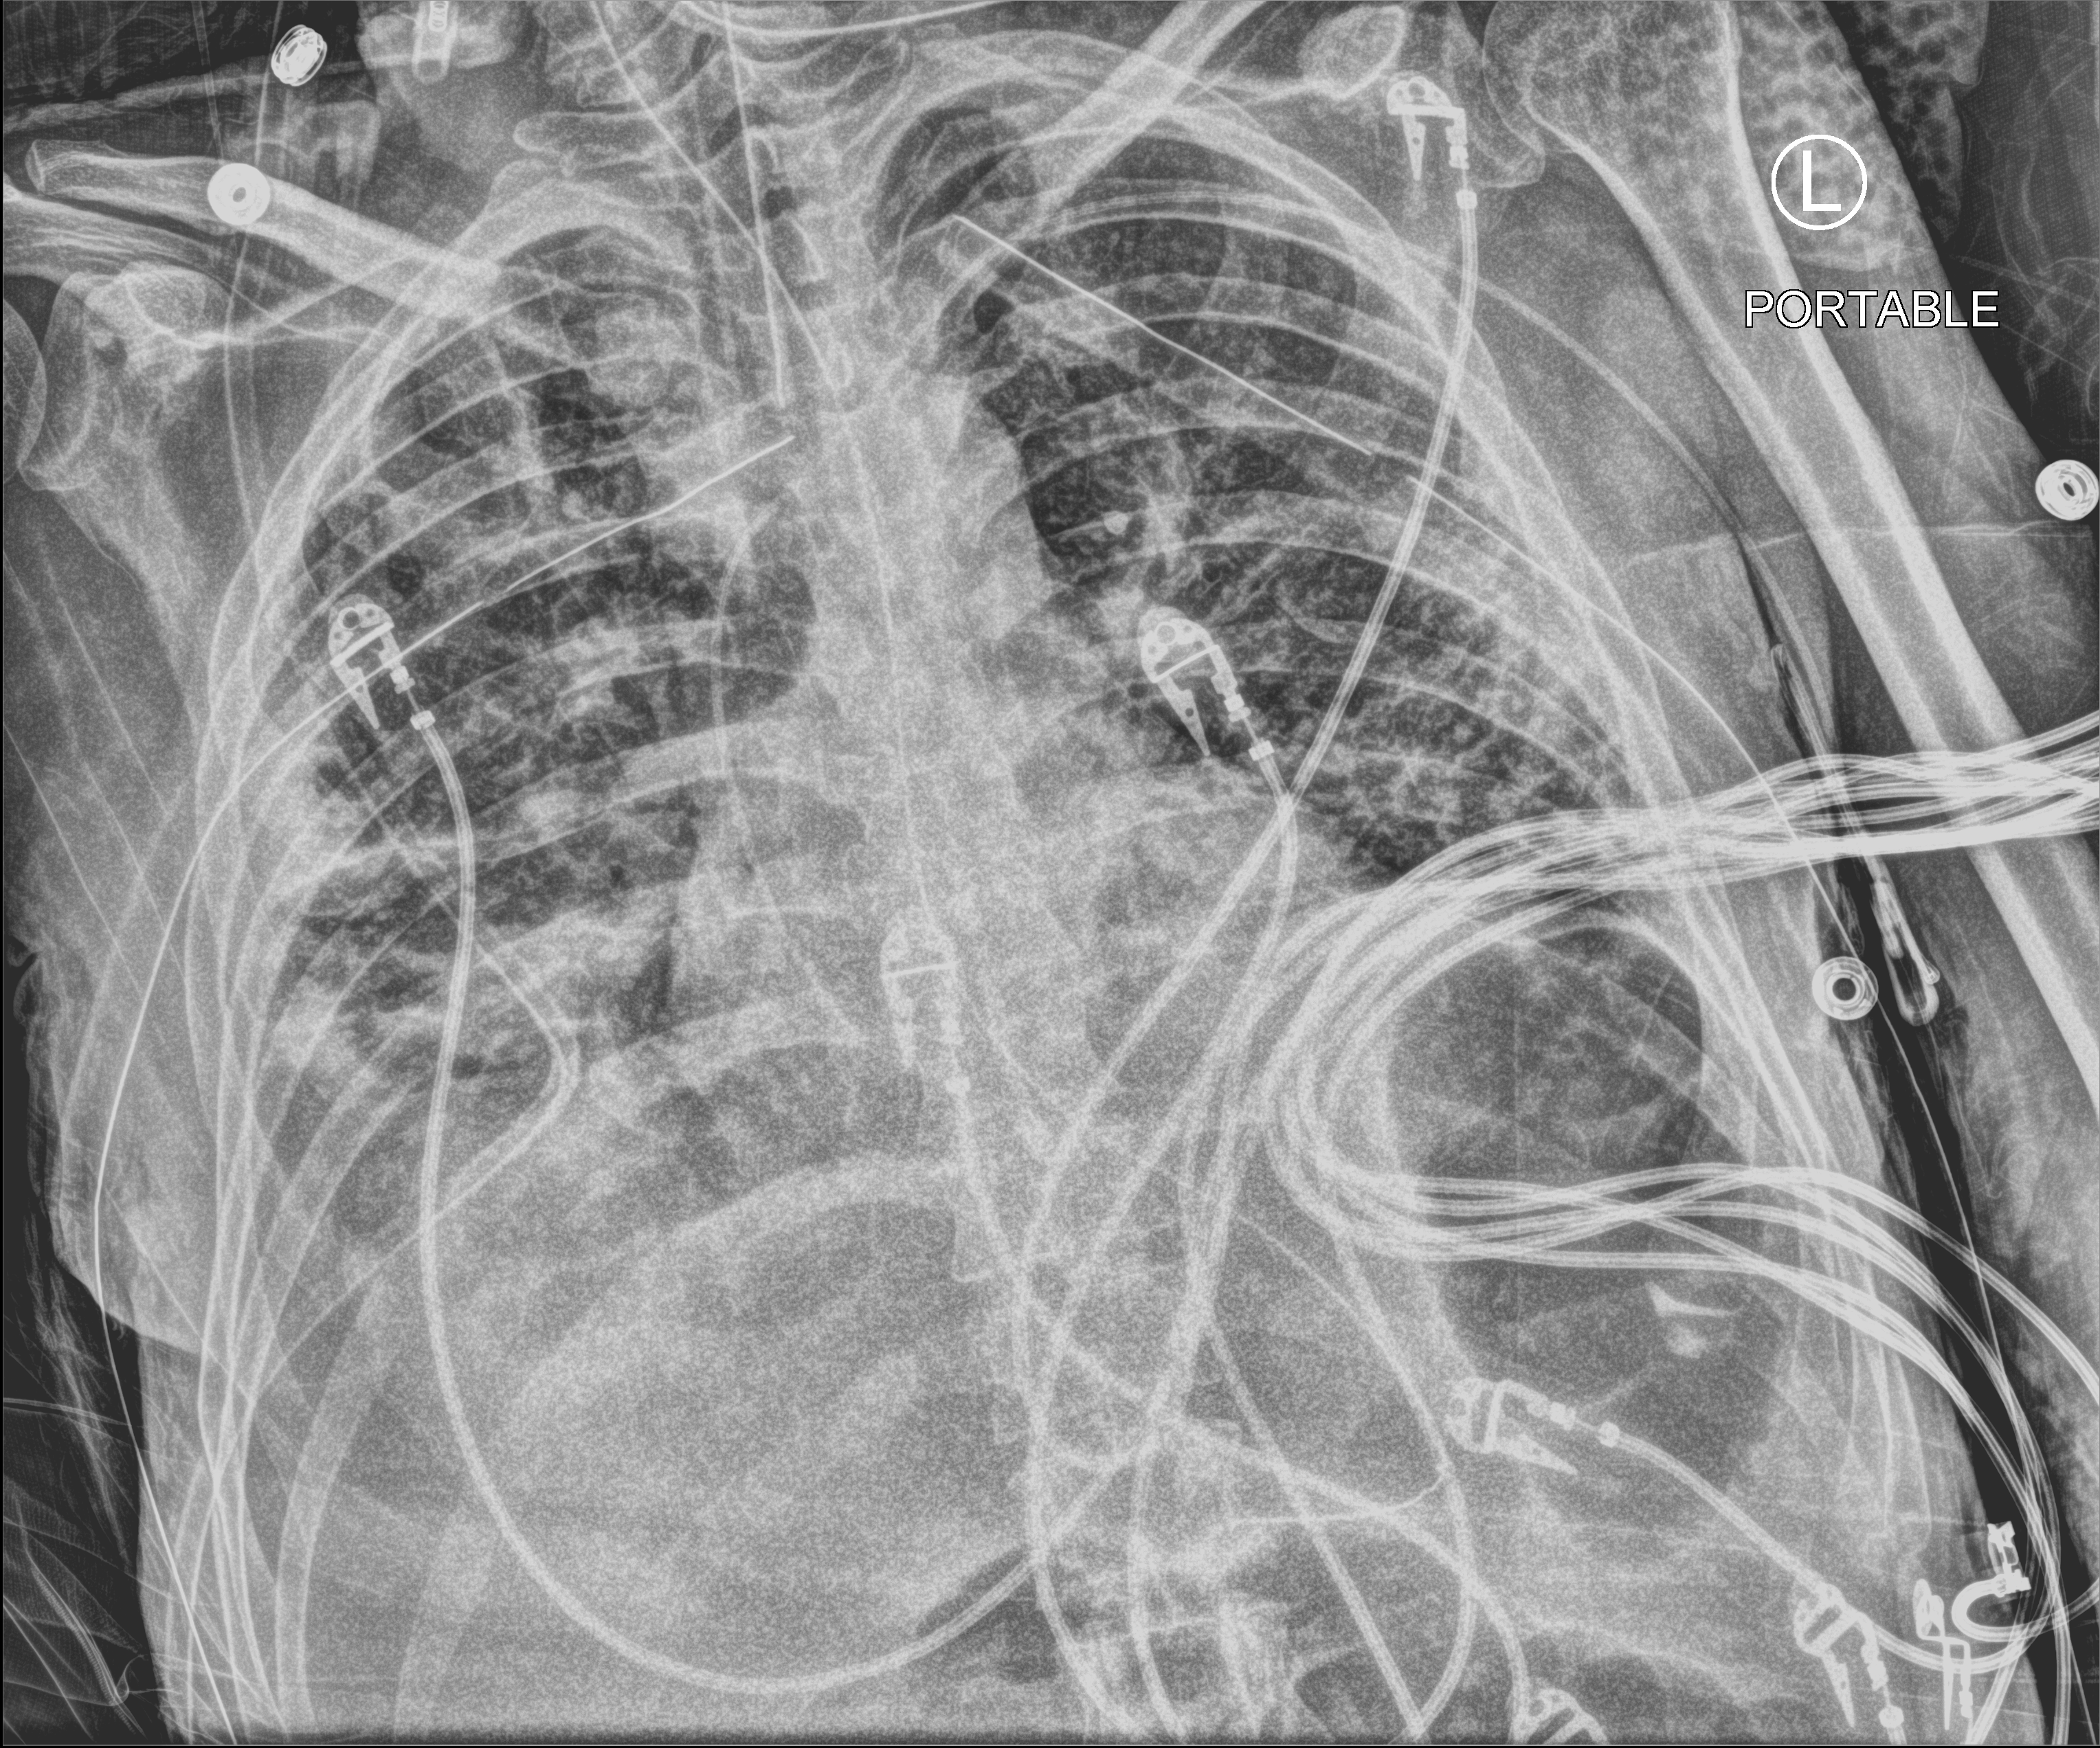
Portable chest radiograph, anteroposterior (AP) projection. Patient hospitalised with COVID-19; male, aged 18–59 years.
Admission-level facts for this patient (not findings on this image; timing relative to this image not recorded): mechanically ventilated during this hospital stay: yes; diabetes (admission record): yes.